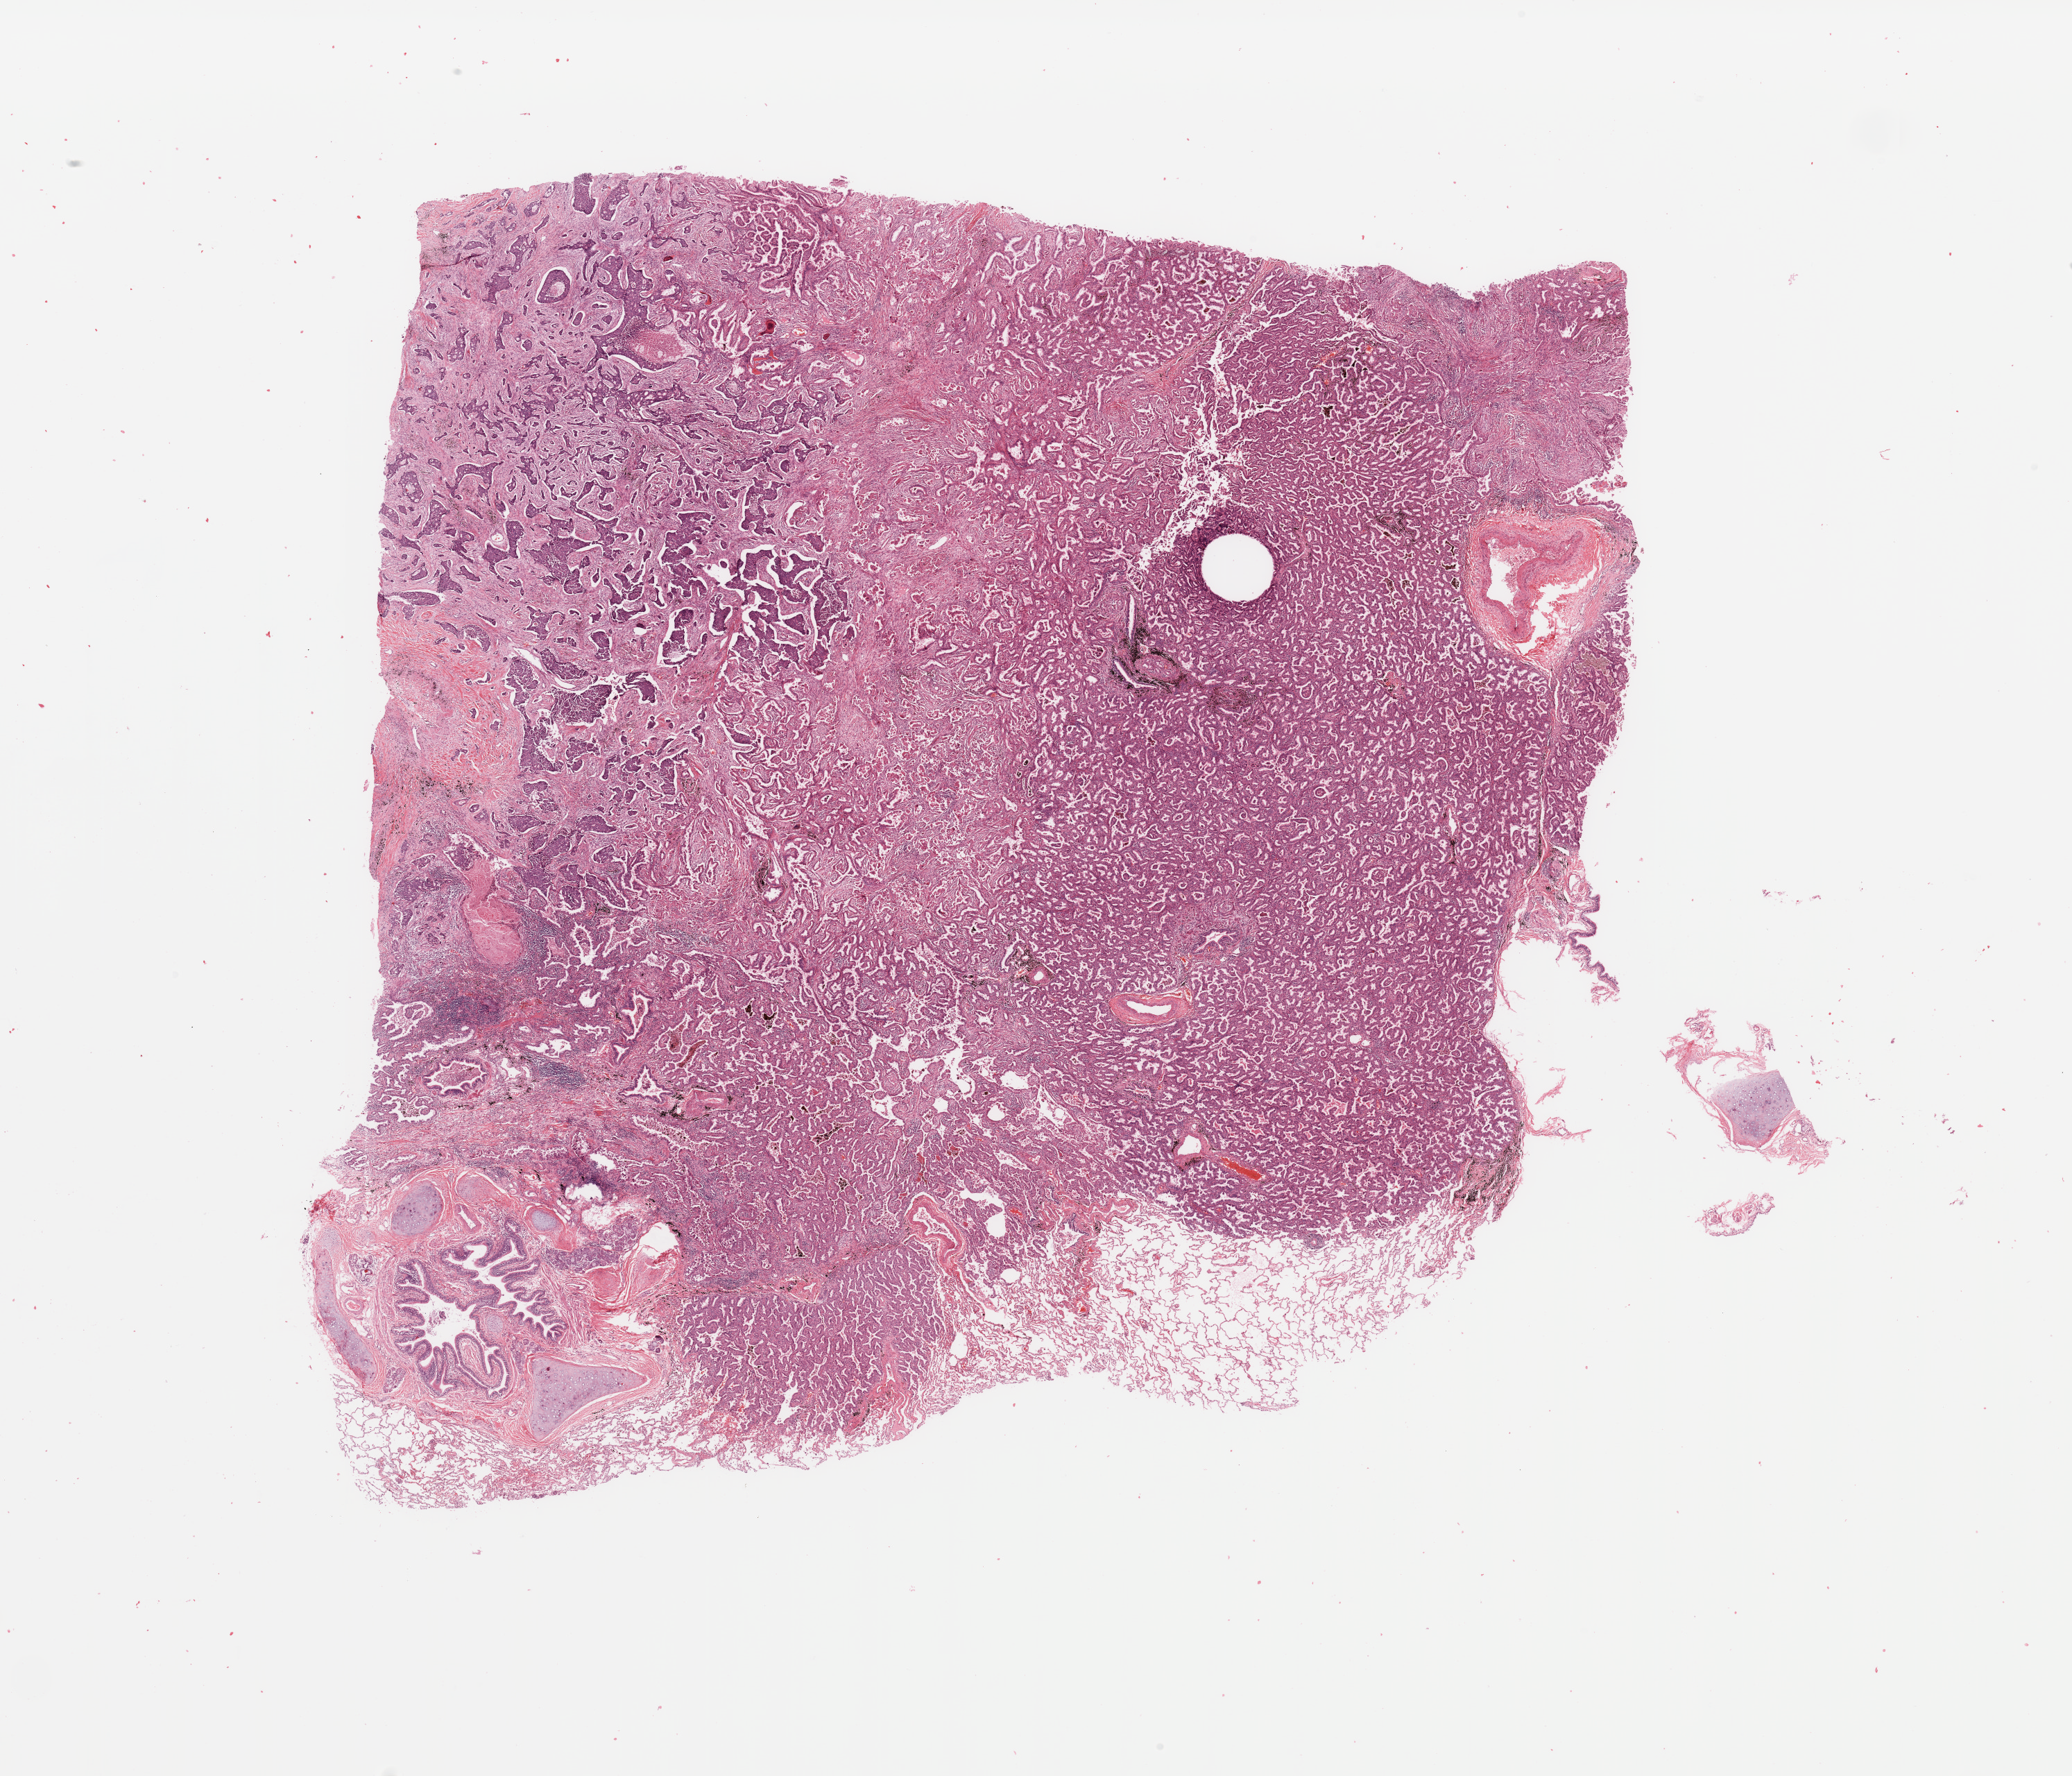
Whole-slide histology image, Hematoxylin and eosin (H&E) stained — low-resolution overview of the scanned area, about 23.6 x 20.2 mm (acquisition: 20x scan), tumour tissue sample, sampled site: lung. Female, 68 y/o. Histologic grade: G2 (moderately differentiated). Composition of this section per pathologist review: tumour nuclei 70%, necrosis 3%.
- diagnosis: Adenocarcinoma, NOS
- AJCC pathologic stage: IB